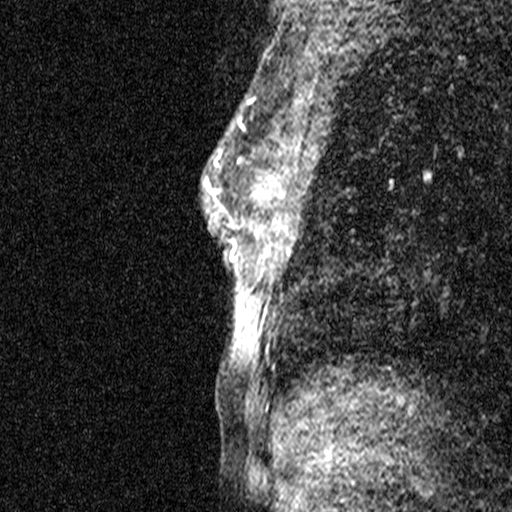
Breast MRI (dynamic contrast-enhanced), one sagittal slice. Slice 24 of 44 in the series (ordered by position). Dynamic contrast-enhanced study with each time point stored as its own series, time point 2 of 3 at this slice position (early post-contrast, ordered by acquisition time). 1.5 T. TE 4.5 ms, TR 11 ms. 3 mm slice thickness. 512 × 512 image matrix, field of view 200 × 200 mm. Patient: female, 44 years. Case-level facts recorded for this patient, not image findings: setting: breast cancer imaged before/during neoadjuvant chemotherapy; receptor status: HR-positive, HER2-negative.
Outlined on this slice (semi-automatic segmentation, software-assisted and operator-edited):
- analysis volume of interest (the breast-tissue region the enhancement analysis was run in; not a lesion): bounding box (x1, y1, x2, y2) in pixels: (218, 118, 277, 291)
- tumour enhancement mask (voxels above the 90 % enhancement threshold inside the analysis volume of interest): (218, 119, 275, 198)